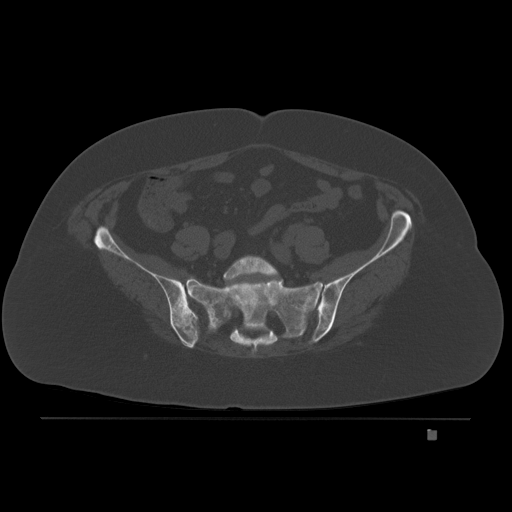
CT including the spine, one axial slice. Slice 23 of 221 in the series (ordered by position). Bone window (W 1800 / L 400 HU). 3 mm slice thickness. 512 × 512 image matrix, field of view 474 × 474 mm. Female patient, age 63 years. From the clinical record (not read from this slice): primary cancer: breast.
Structures marked on this image (semi-automatically segmented with operator editing):
- L5 vertebra: bounding box [x1, y1, x2, y2] px = [223, 255, 279, 282]